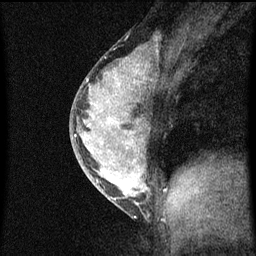
Breast MRI (dynamic contrast-enhanced), one sagittal slice; position 33 of 60 along the scan axis; dynamic contrast-enhanced series, image 2 of 3 at this slice position (ordered by acquisition); 1.5 T; TE 4.2 ms, TR 8 ms; 2 mm slice thickness; 256 × 256 image matrix, field of view 180 × 180 mm. Female patient, age 33 years.
Outlined on this slice (semi-automatically segmented with operator editing):
- analysis volume of interest (the breast-tissue region the enhancement analysis was run in; not a lesion): bounding box [x1, y1, x2, y2] px = [70, 56, 159, 215]
- tumour enhancement mask (voxels above the 70 % enhancement threshold inside the analysis volume of interest): [76, 70, 149, 205]